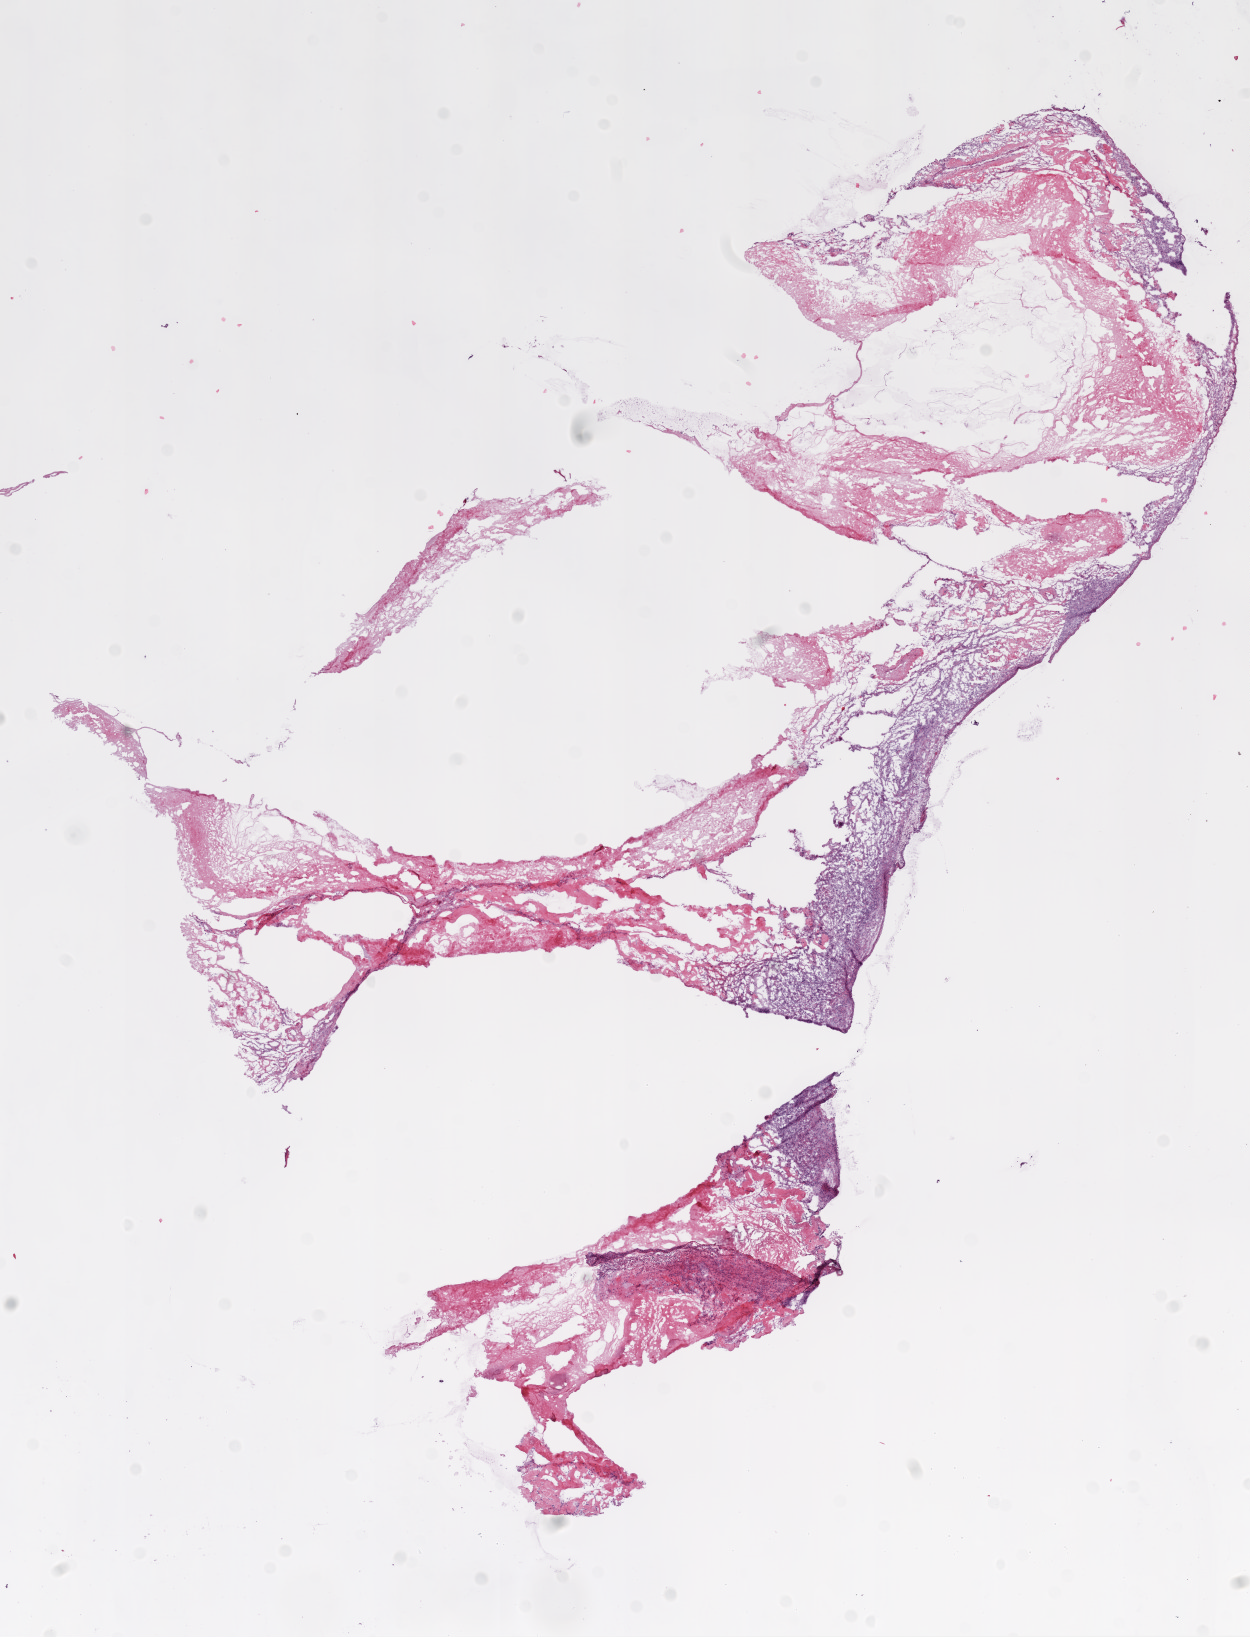
H&E whole-slide image — low-resolution overview of the scanned area, about 10.0 x 13.1 mm. Frozen section from the top of the tissue portion. Ovary, solid tissue normal (non-tumour tissue) sample. Female patient; age at initial diagnosis 74 years.
This section: solid tissue normal (non-tumour) sample from the same patient. Patient diagnosis: Serous cystadenocarcinoma, NOS.